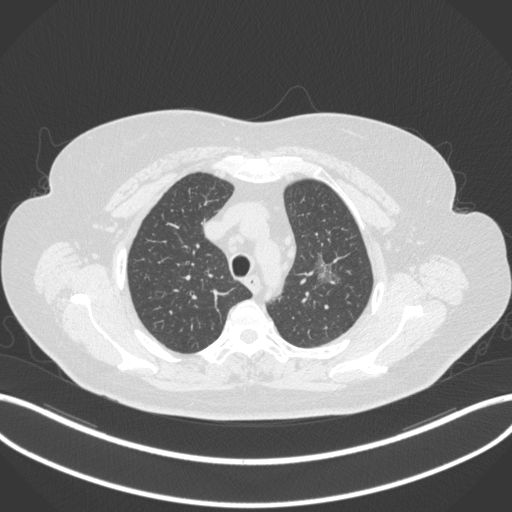
Chest CT, one axial slice; slice 264 of 310 in the series (ordered by position); reconstruction kernel B31f; 120 kVp; lung window (W 1500 / L -600 HU); 1 mm slice thickness; 512 × 512 image matrix. Female patient, age 70 years. From the clinical record (not read from this slice): clinical TNM (as recorded): T1c N0 M0.
Structures marked on this image (rectangle marked by the reading radiologist):
- lung tumour (recorded histology: adenocarcinoma): box from (x=312, y=251) to (x=344, y=290) px